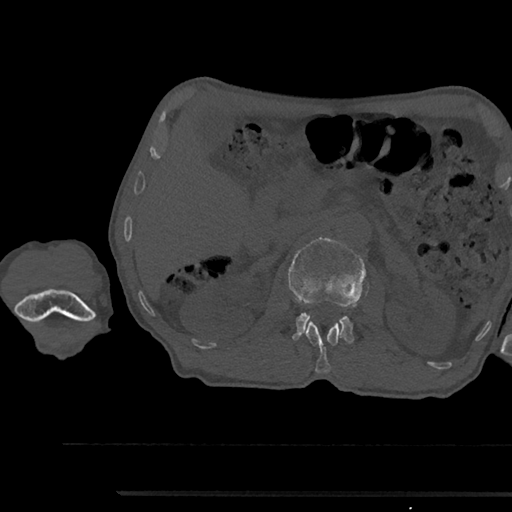
CT including the spine, one axial slice; position 602 of 797 along the scan axis; reconstruction kernel Br40s/3; 120 kVp; bone window (W 1800 / L 400 HU); 0.5 mm slice thickness; 512 × 512 image matrix, field of view 367 × 367 mm. Male patient, age 79 years. Case-level facts recorded for this patient, not image findings: primary cancer: prostate.
Annotated regions visible in this slice (semi-automatic segmentation, software-assisted and operator-edited):
- L1 vertebra: bounding box [x1, y1, x2, y2] px = [305, 321, 342, 373]
- L2 vertebra: [288, 237, 366, 344]